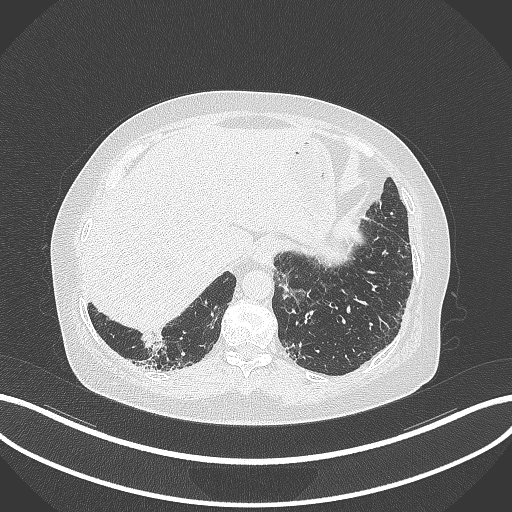
Chest CT, one axial slice; slice 15 of 296 in the series (ordered by position); reconstruction kernel B70f; 120 kVp; lung window (W 1500 / L -600 HU); 512 × 512 image matrix, field of view 400 × 400 mm. Female patient, age 65 years. Case-level facts recorded for this patient, not image findings: clinical TNM (as recorded): T2b N1 M0; histopathological grade: G1.
Annotated regions visible in this slice (bounding box drawn by a radiologist):
- lung tumour (recorded histology: adenocarcinoma): bounding box [x1, y1, x2, y2] px = [139, 330, 174, 357]